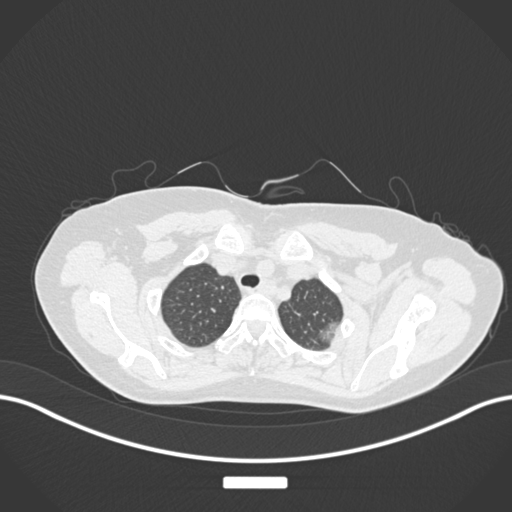
Chest CT, one axial slice. Slice 151 of 181 in the series (ordered by position). Reconstruction kernel B30f. Lung window (W 1500 / L -600 HU). 1 mm slice thickness. 512 × 512 image matrix. Patient: female, 58 years. From the clinical record (not read from this slice): clinical TNM (as recorded): T1c N0 M0.
Structures marked on this image (bounding box drawn by a radiologist):
- lung tumour (recorded histology: adenocarcinoma): bounding box <315,317,345,343> (left, top, right, bottom; pixels)